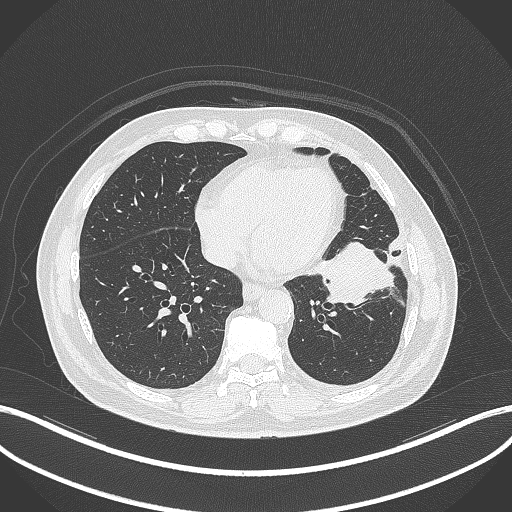
Chest CT, one axial slice; slice 124 of 230 in the series (ordered by position); 120 kVp; lung window (W 1500 / L -600 HU); 1 mm slice thickness; 512 × 512 image matrix. Patient: male, 68 years. From the clinical record (not read from this slice): clinical TNM (as recorded): T2b N0 M0.
Outlined on this slice (bounding box drawn by a radiologist):
- lung tumour (recorded histology: squamous cell carcinoma): bounding box [x1, y1, x2, y2] px = [315, 241, 400, 309]